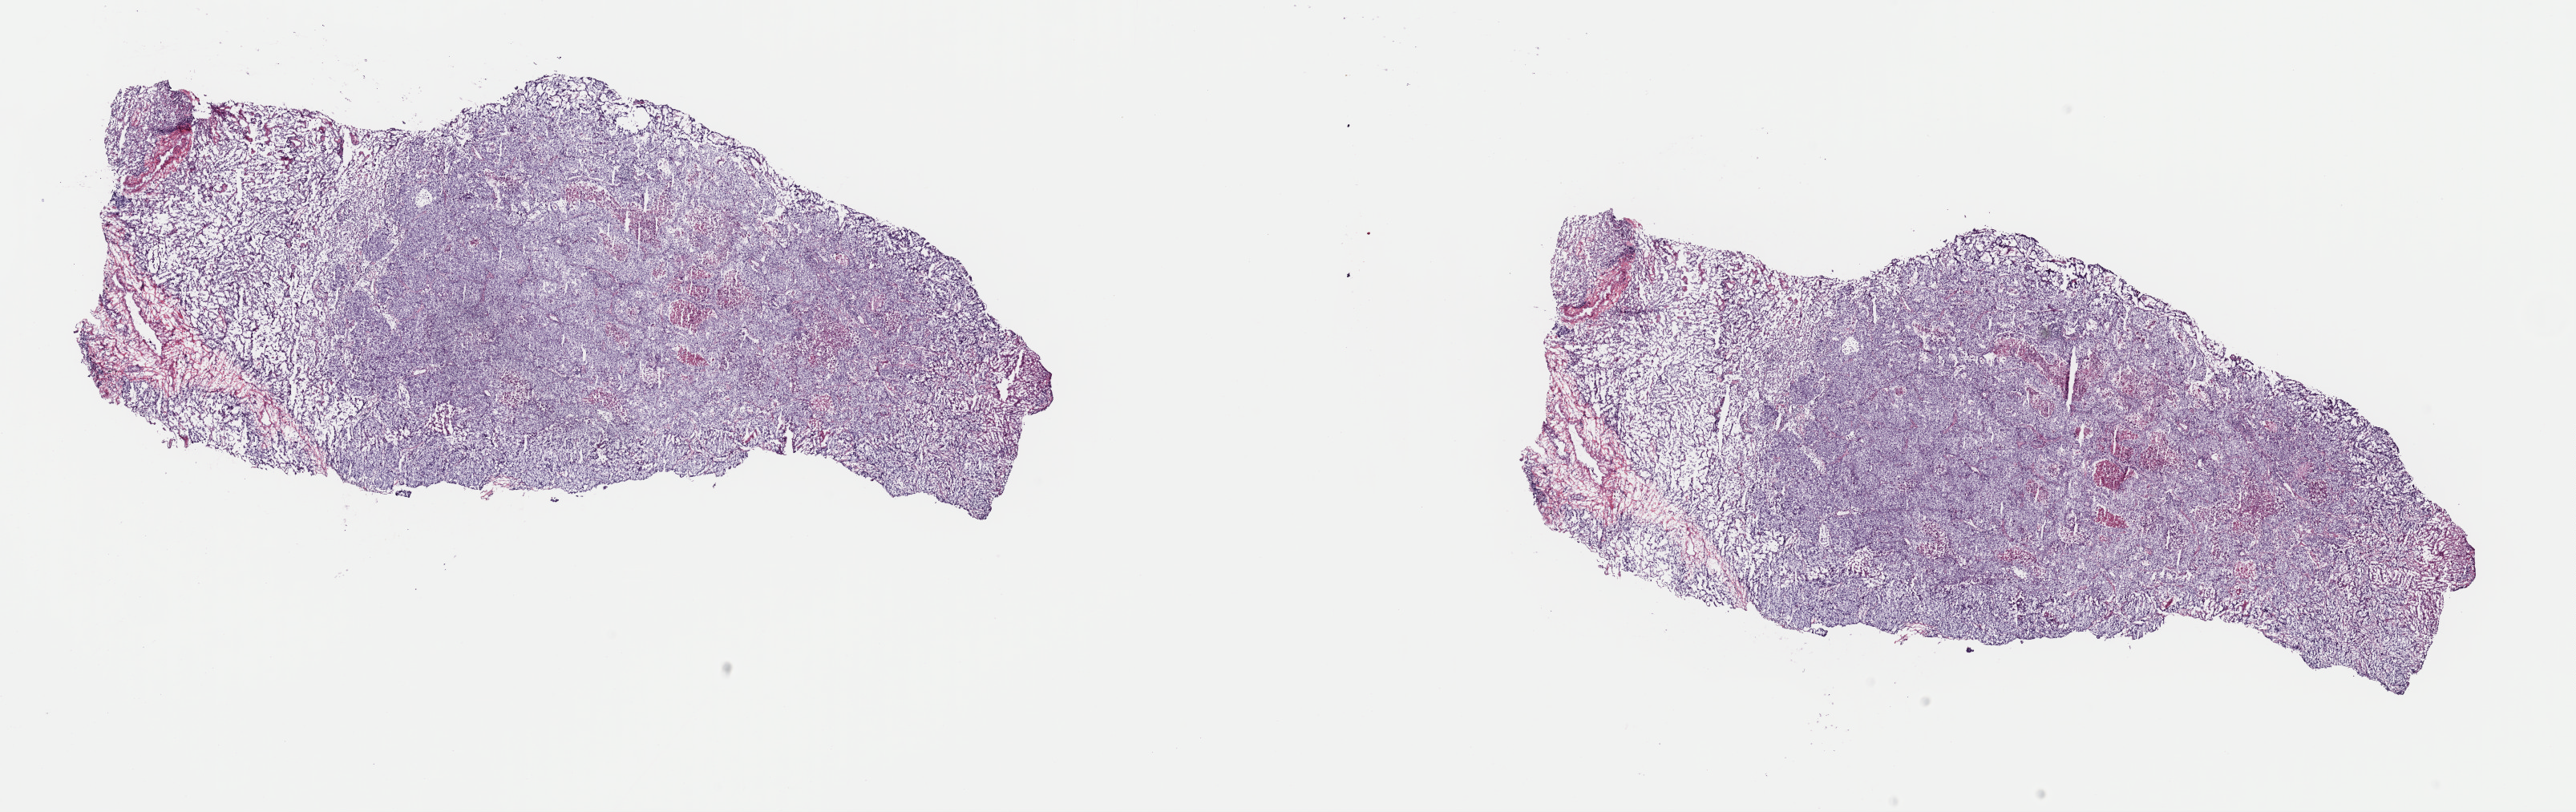
H&E whole-slide image, shown as a low-resolution overview of the whole scanned area (about 25.4 x 8.0 mm, slide scanned at 40x), frozen section from the top of the tissue portion, sample: primary tumour, lung. Male, age 64 years at initial diagnosis. Slide review estimates, as recorded: tumour cells 70%, tumour nuclei 70%, normal cells 30%, stromal cells 0%, necrosis 0%. Infiltration values recorded for this section: lymphocyte infiltration 2%, monocyte infiltration 2%, neutrophil infiltration 0%.
• laterality: left
• TNM: T2b N1 M0
• AJCC pathologic stage: IIB (7th edition)
• diagnosis: Adenocarcinoma, NOS (upper lobe, lung)